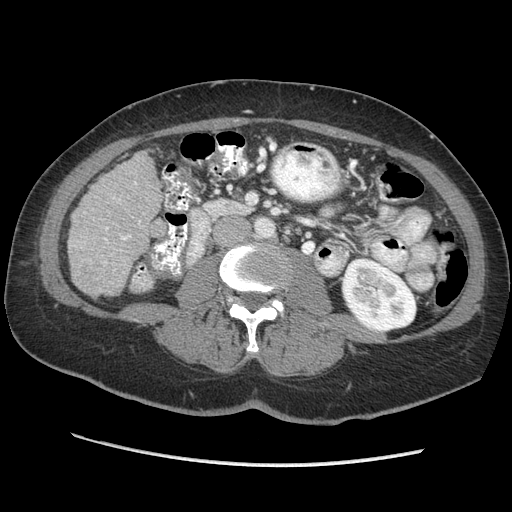
Contrast-enhanced abdominal CT (liver protocol), one axial slice; reconstruction kernel STANDARD; 140 kVp; soft-tissue window (W 400 / L 40 HU); 512 × 512 image matrix, field of view 360 × 360 mm. From the clinical record (not read from this slice): diagnosis: hepatocellular carcinoma (patient treated with transarterial chemoembolisation; whether this scan precedes or follows treatment is not stated here); TNM stage (as recorded): Stage-II; Child-Pugh class: A; tumour nodularity: multinodular; tumour size: 4 cm.
Annotated regions visible in this slice (semi-automatically segmented with operator editing):
- liver parenchyma outside the tumour (the mass and vessels are separate outlines, so this box may not span the whole liver): box from (x=68, y=150) to (x=162, y=296) px
- liver vessels: (x=104, y=182)–(x=140, y=240)